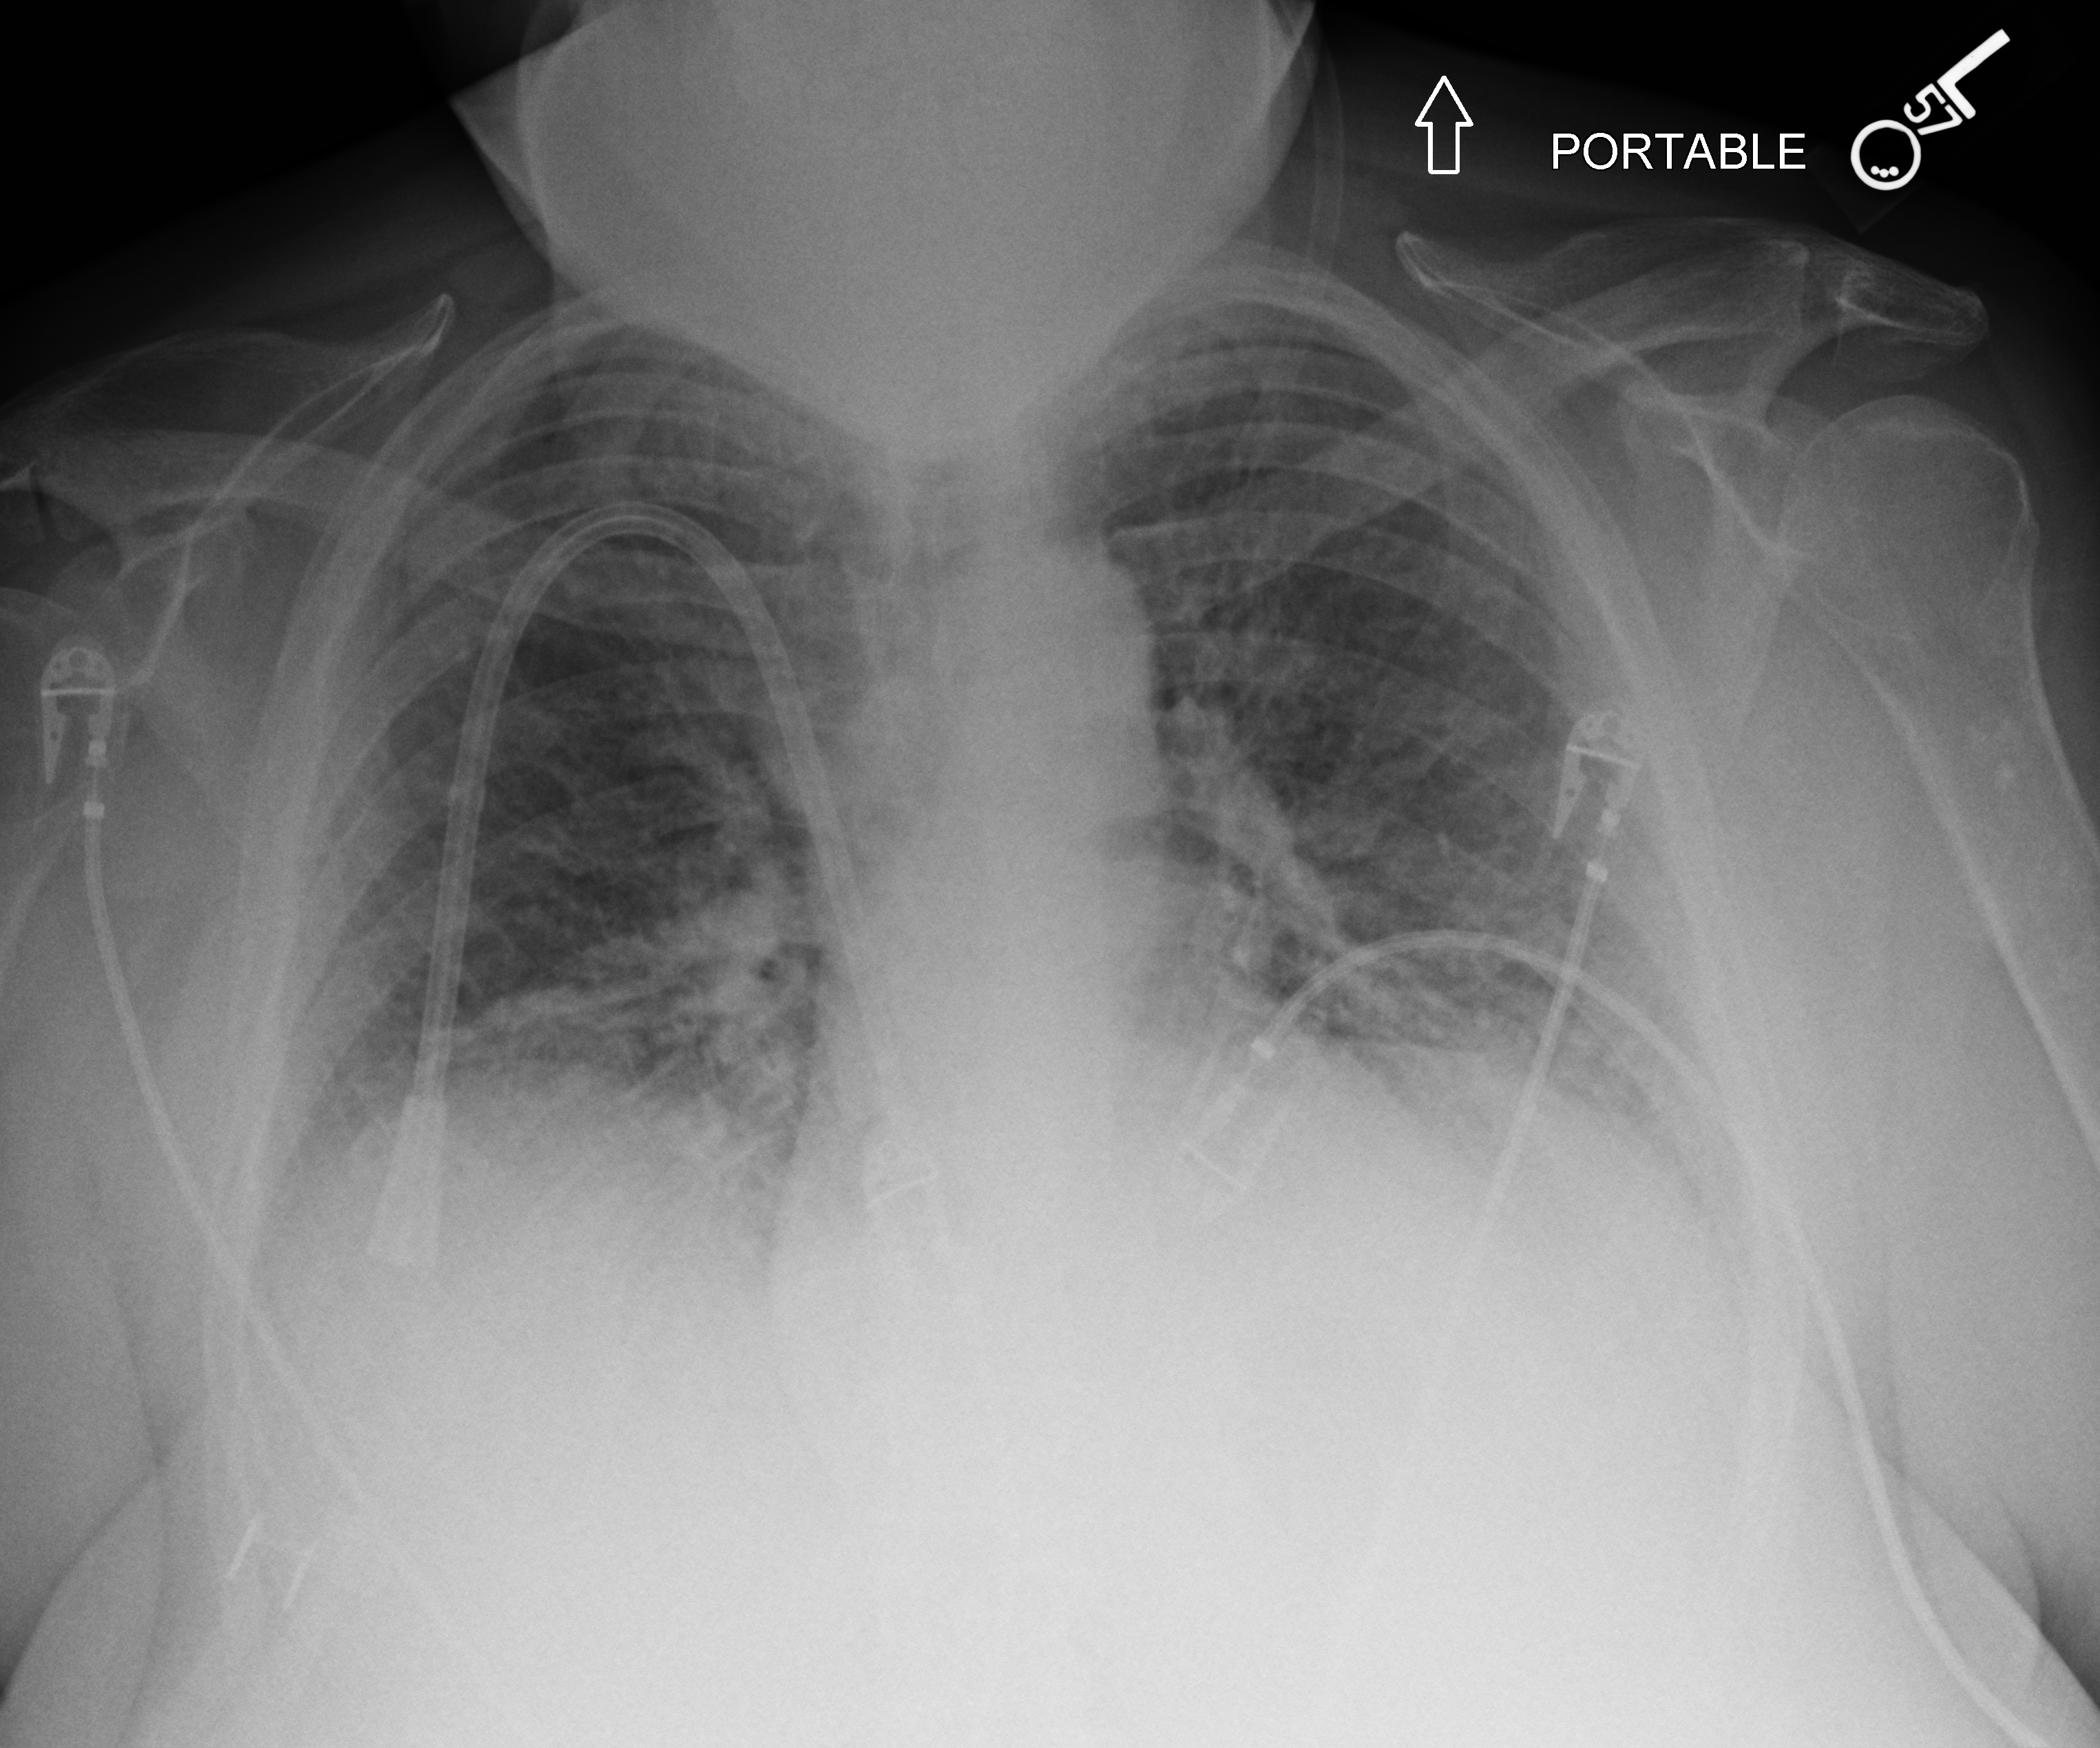
Bedside chest radiograph (computed radiography), anteroposterior (AP) projection. Patient hospitalised with COVID-19; female, aged 60–74 years.
From the hospital-stay record, not from the radiograph (when in the stay this image was taken is not recorded): admitted to intensive care during this hospital stay: no; mechanically ventilated during this hospital stay: no.